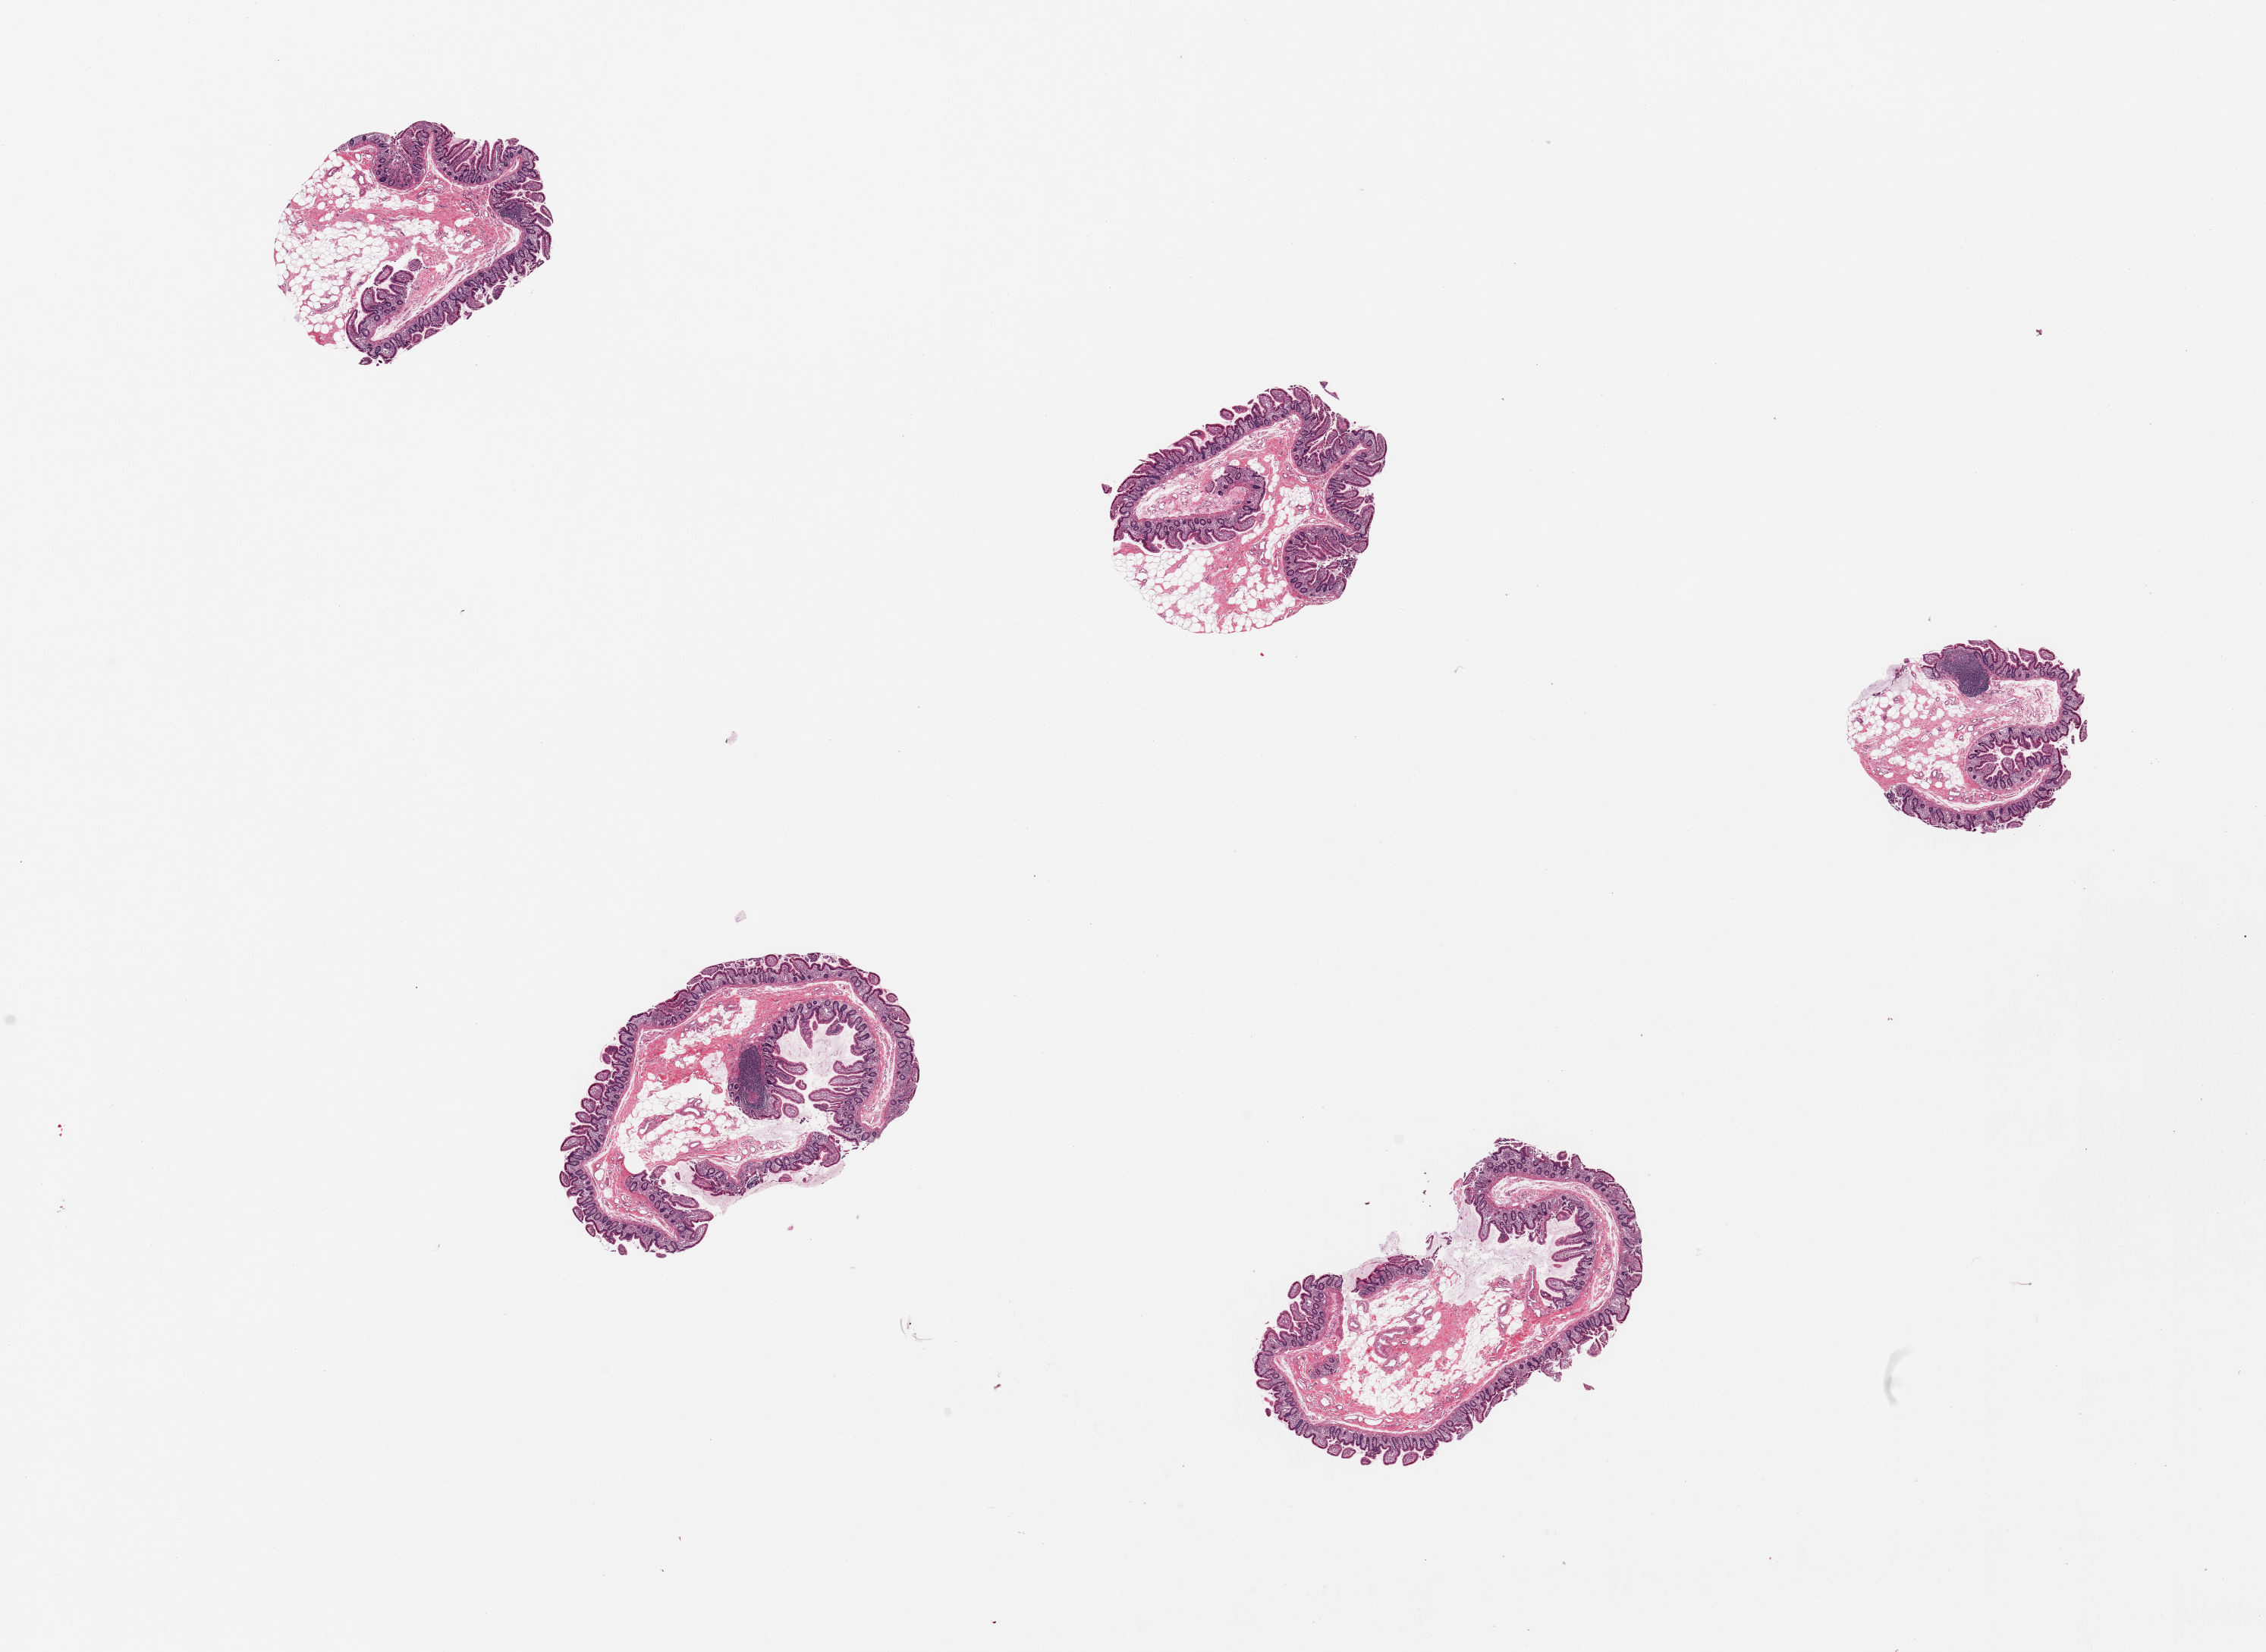
Digitized H&E-stained section, low-resolution overview of the scanned area, about 23.6 x 17.2 mm. PAXgene-fixed paraffin-embedded (PFPE) section. Sampled site (target tissue): ileum. Tissue donor sample. Donor: female.
• reviewer comment on this tissue sample: 4 pieces, well preserved mucosa, lymphoid aggregates are ~5% total